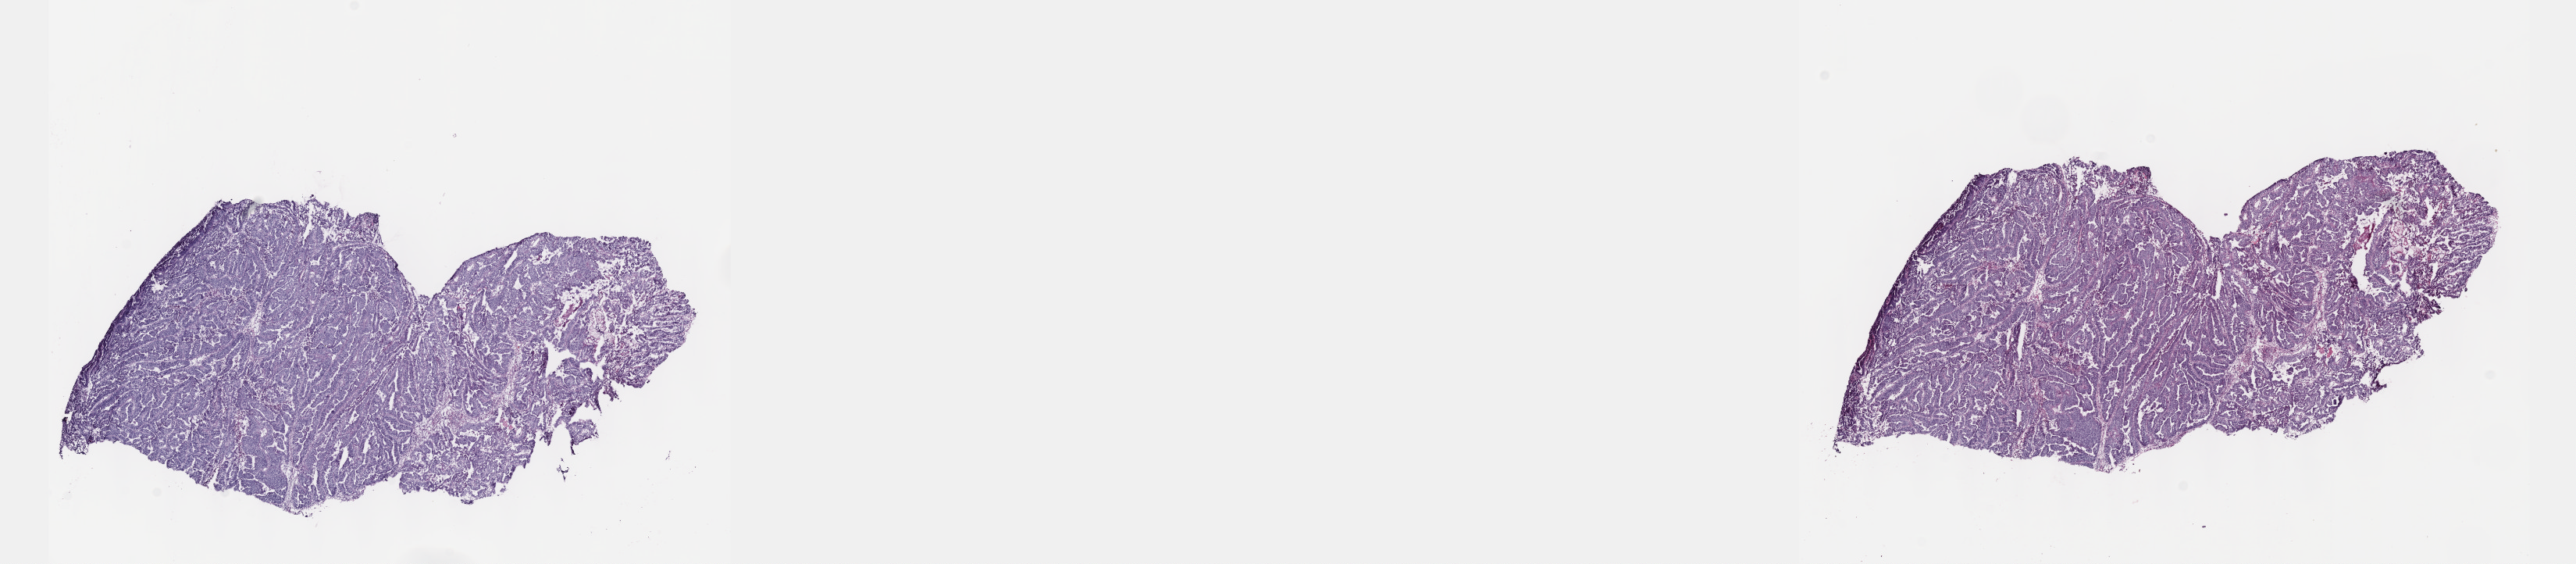
Whole-slide histology image, Hematoxylin and eosin (H&E) stained — low-resolution overview of the scanned area, about 26.7 x 5.8 mm (acquisition: 40x scan). Frozen section from the top of the tissue portion. Primary tumour sample from the uterus. Female patient; age at initial diagnosis 71 years. Histologic grade: G3 (poorly differentiated). Slide review estimates, as recorded: tumour cells 80%, tumour nuclei 80%, normal cells 0%, stromal cells 10%, necrosis 10%. Inflammatory infiltration, as recorded: lymphocyte infiltration 40%, monocyte infiltration 20%, neutrophil infiltration 20%.
- pathologic diagnosis: Serous cystadenocarcinoma, NOS (endometrium)
- FIGO stage: IA